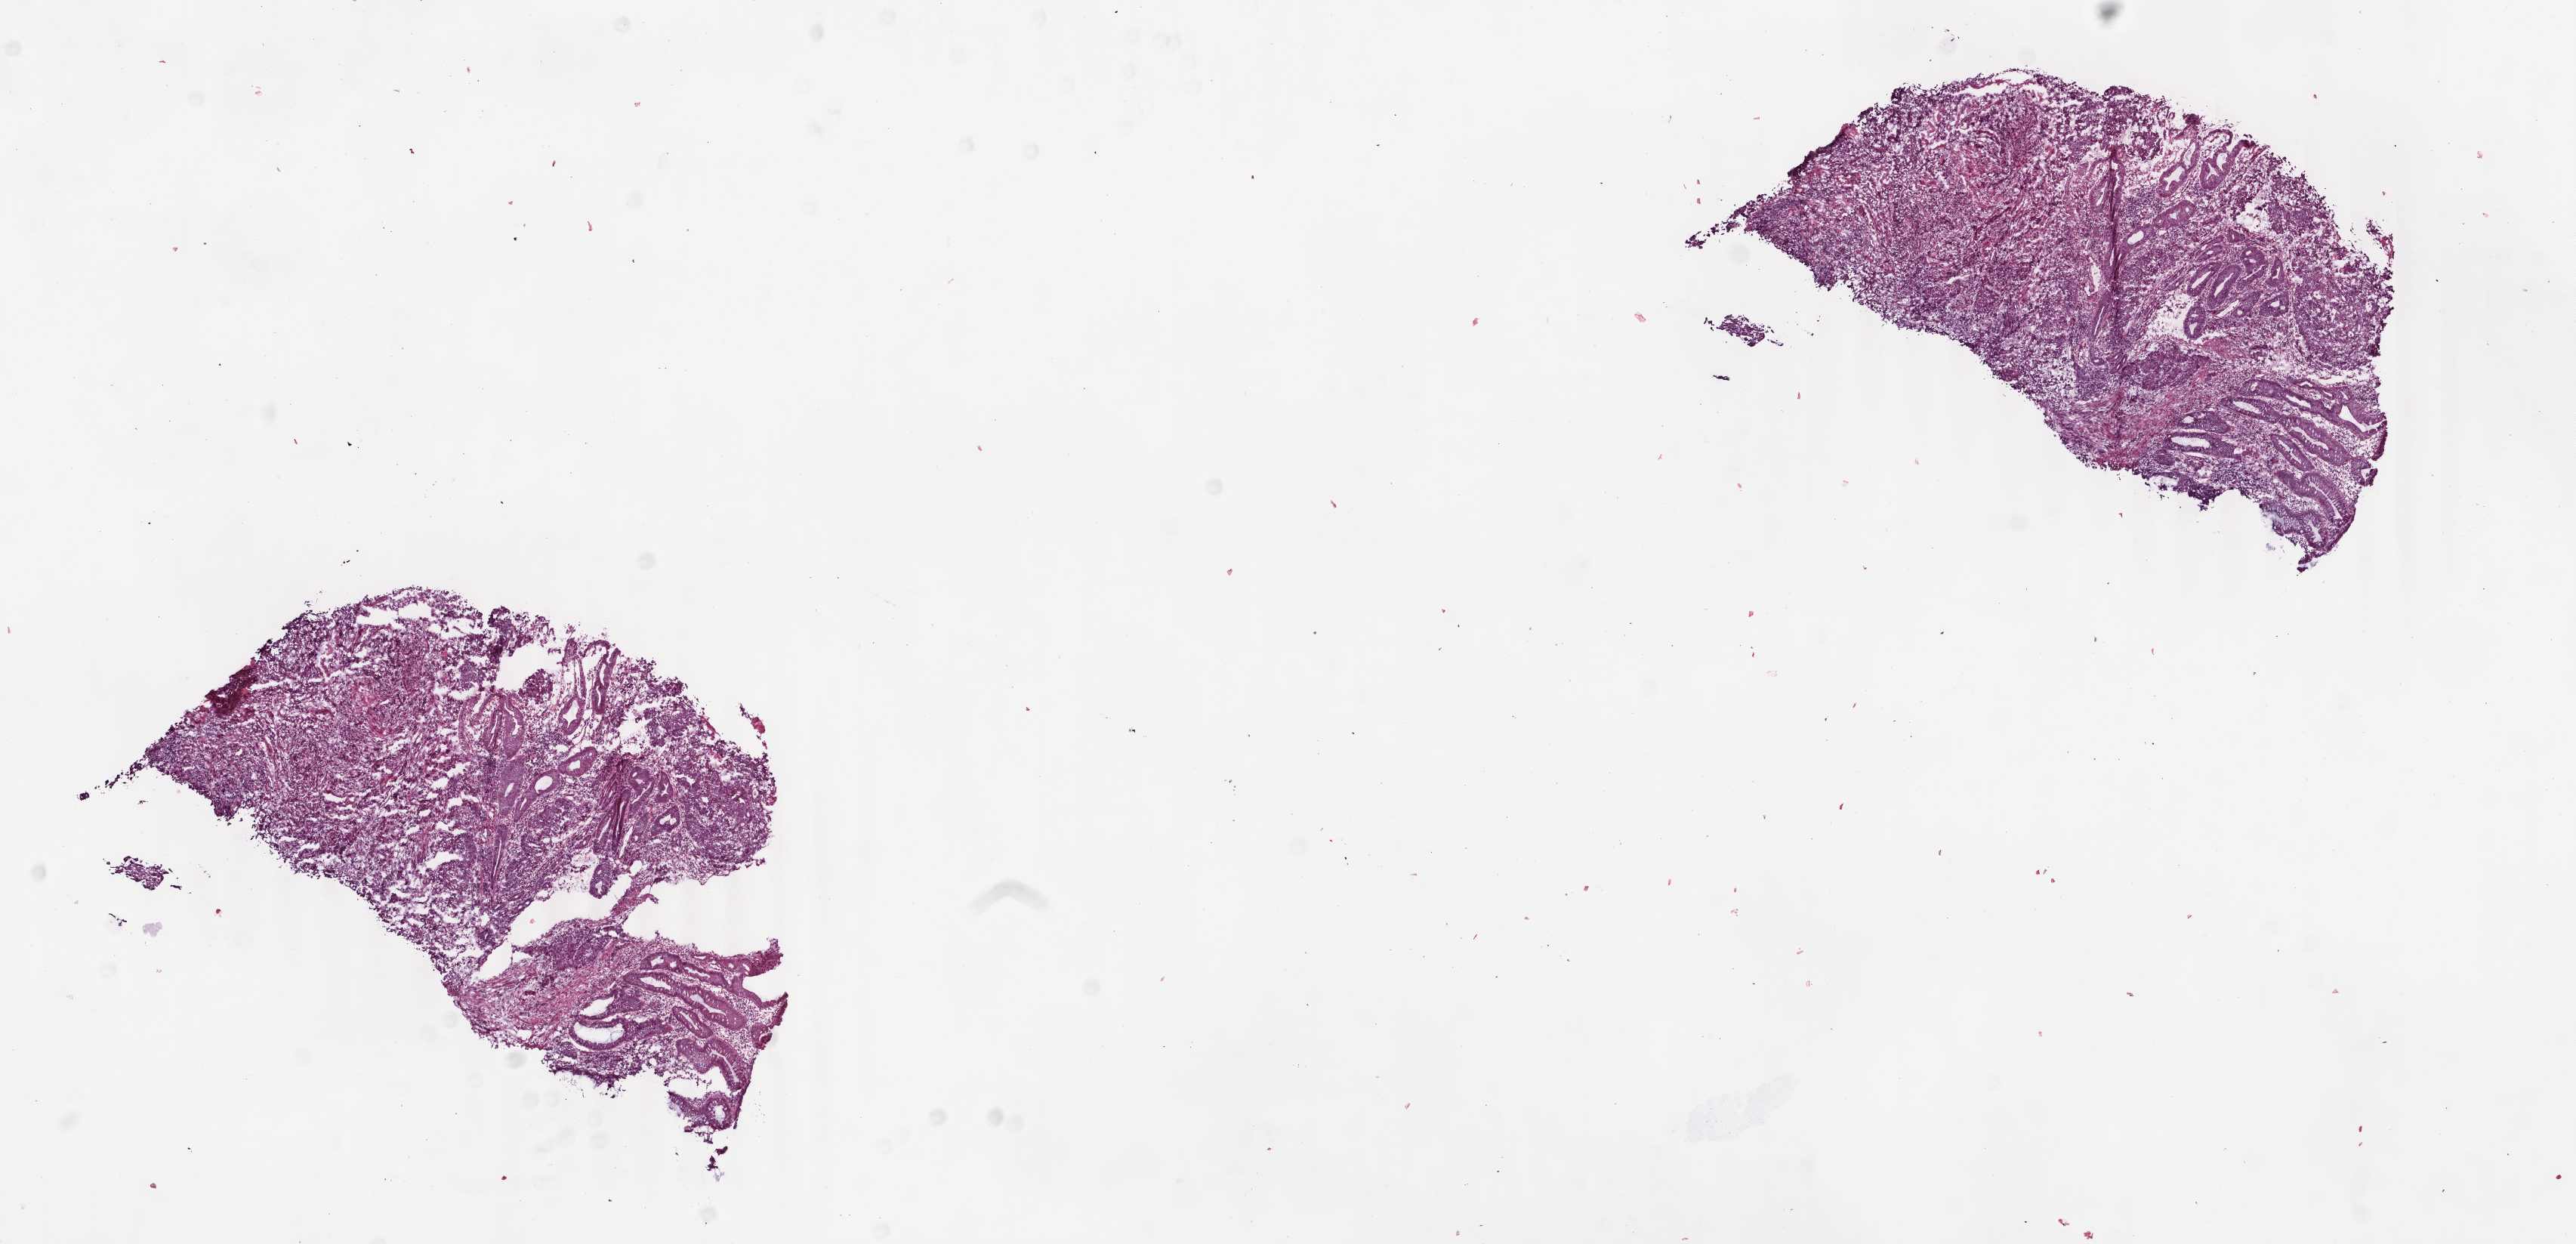
Digitized H&E tissue section (whole slide), whole scanned area (about 13.6 x 6.5 mm, acquisition: 40x scan) shown as a low-resolution overview, frozen section, sample: primary tumour, rectum. Male, age 80 years at initial diagnosis. Pathologist review of this section (percent, as recorded): tumour cells 80%, tumour nuclei 60%, normal cells 0%, stromal cells 19%, necrosis 1%. Infiltration values recorded for this section: lymphocyte infiltration 15%, monocyte infiltration 15%, neutrophil infiltration 3%.
TNM: T3 N0 M0. AJCC pathologic stage: IIA (6th edition). Lymph nodes positive (case pathology): 0 of 14 examined. Diagnosis: Adenocarcinoma, NOS.